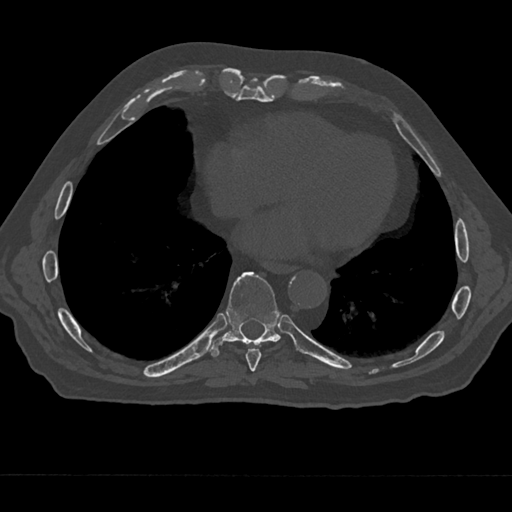
CT including the spine, one axial slice. Slice 283 of 797 in the series (ordered by position). Reconstruction kernel Br40s/3. Bone window (W 1800 / L 400 HU). 0.5 mm slice thickness. 512 × 512 image matrix. Patient: male, 75 years. From the clinical record (not read from this slice): primary cancer: renal; vertebrae with lytic lesions (as recorded): T4.
Structures marked on this image (semi-automatically segmented with operator editing):
- T8 vertebra: bounding box [x1, y1, x2, y2] px = [246, 348, 261, 371]
- T9 vertebra: [210, 272, 295, 356]